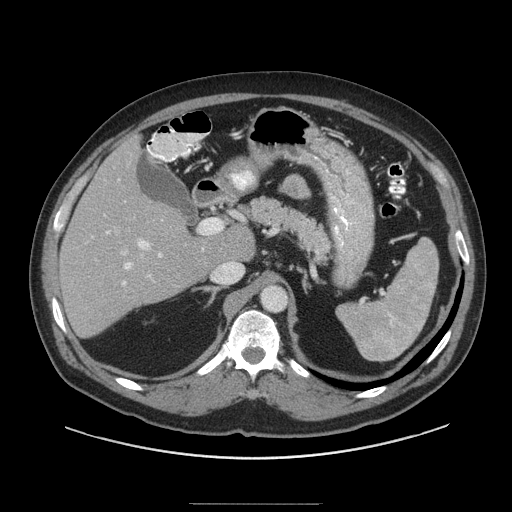
Contrast-enhanced abdominal CT (liver protocol), one axial slice. Slice 58 of 91 in the series (ordered by position). 140 kVp. Soft-tissue window (W 400 / L 40 HU). 2.5 mm slice thickness. 512 × 512 image matrix, field of view 440 × 440 mm. Case-level facts recorded for this patient, not image findings: diagnosis: hepatocellular carcinoma (patient treated with transarterial chemoembolisation; whether this scan precedes or follows treatment is not stated here); TNM stage (as recorded): Stage-I.
Annotated regions visible in this slice (semi-automatic segmentation, software-assisted and operator-edited):
- liver parenchyma outside the tumour (the mass and vessels are separate outlines, so this box may not span the whole liver): bounding box (x1, y1, x2, y2) in pixels: (58, 135, 254, 336)
- liver vessels: (106, 231, 204, 285)